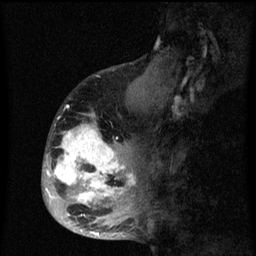
Breast MRI (dynamic contrast-enhanced), one sagittal slice. Position 25 of 60 along the scan axis. Dynamic contrast-enhanced series, image 2 of 3 at this slice position (ordered by acquisition). 1.5 T. TE 4.2 ms, TR 8 ms. 2 mm slice thickness. 256 × 256 image matrix. Patient: female, 50 years.
Annotated regions visible in this slice (semi-automatic segmentation, software-assisted and operator-edited):
- analysis volume of interest (the breast-tissue region the enhancement analysis was run in; not a lesion): bounding box [x1, y1, x2, y2] px = [43, 90, 142, 216]
- tumour enhancement mask (voxels above the 70 % enhancement threshold inside the analysis volume of interest): [45, 114, 136, 216]